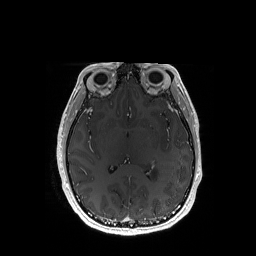
Brain MRI from a brain-tumour surgery series, one axial slice; slice 89 of 192 in the series (ordered by position); T1-weighted post-contrast; 256 × 256 image matrix. From the clinical record (not read from this slice): histopathology: Astrocytoma; WHO grade: 3; IDH mutation: yes.
Outlined on this slice (manually delineated by an expert):
- tumour: box from (x=152, y=169) to (x=158, y=180) px